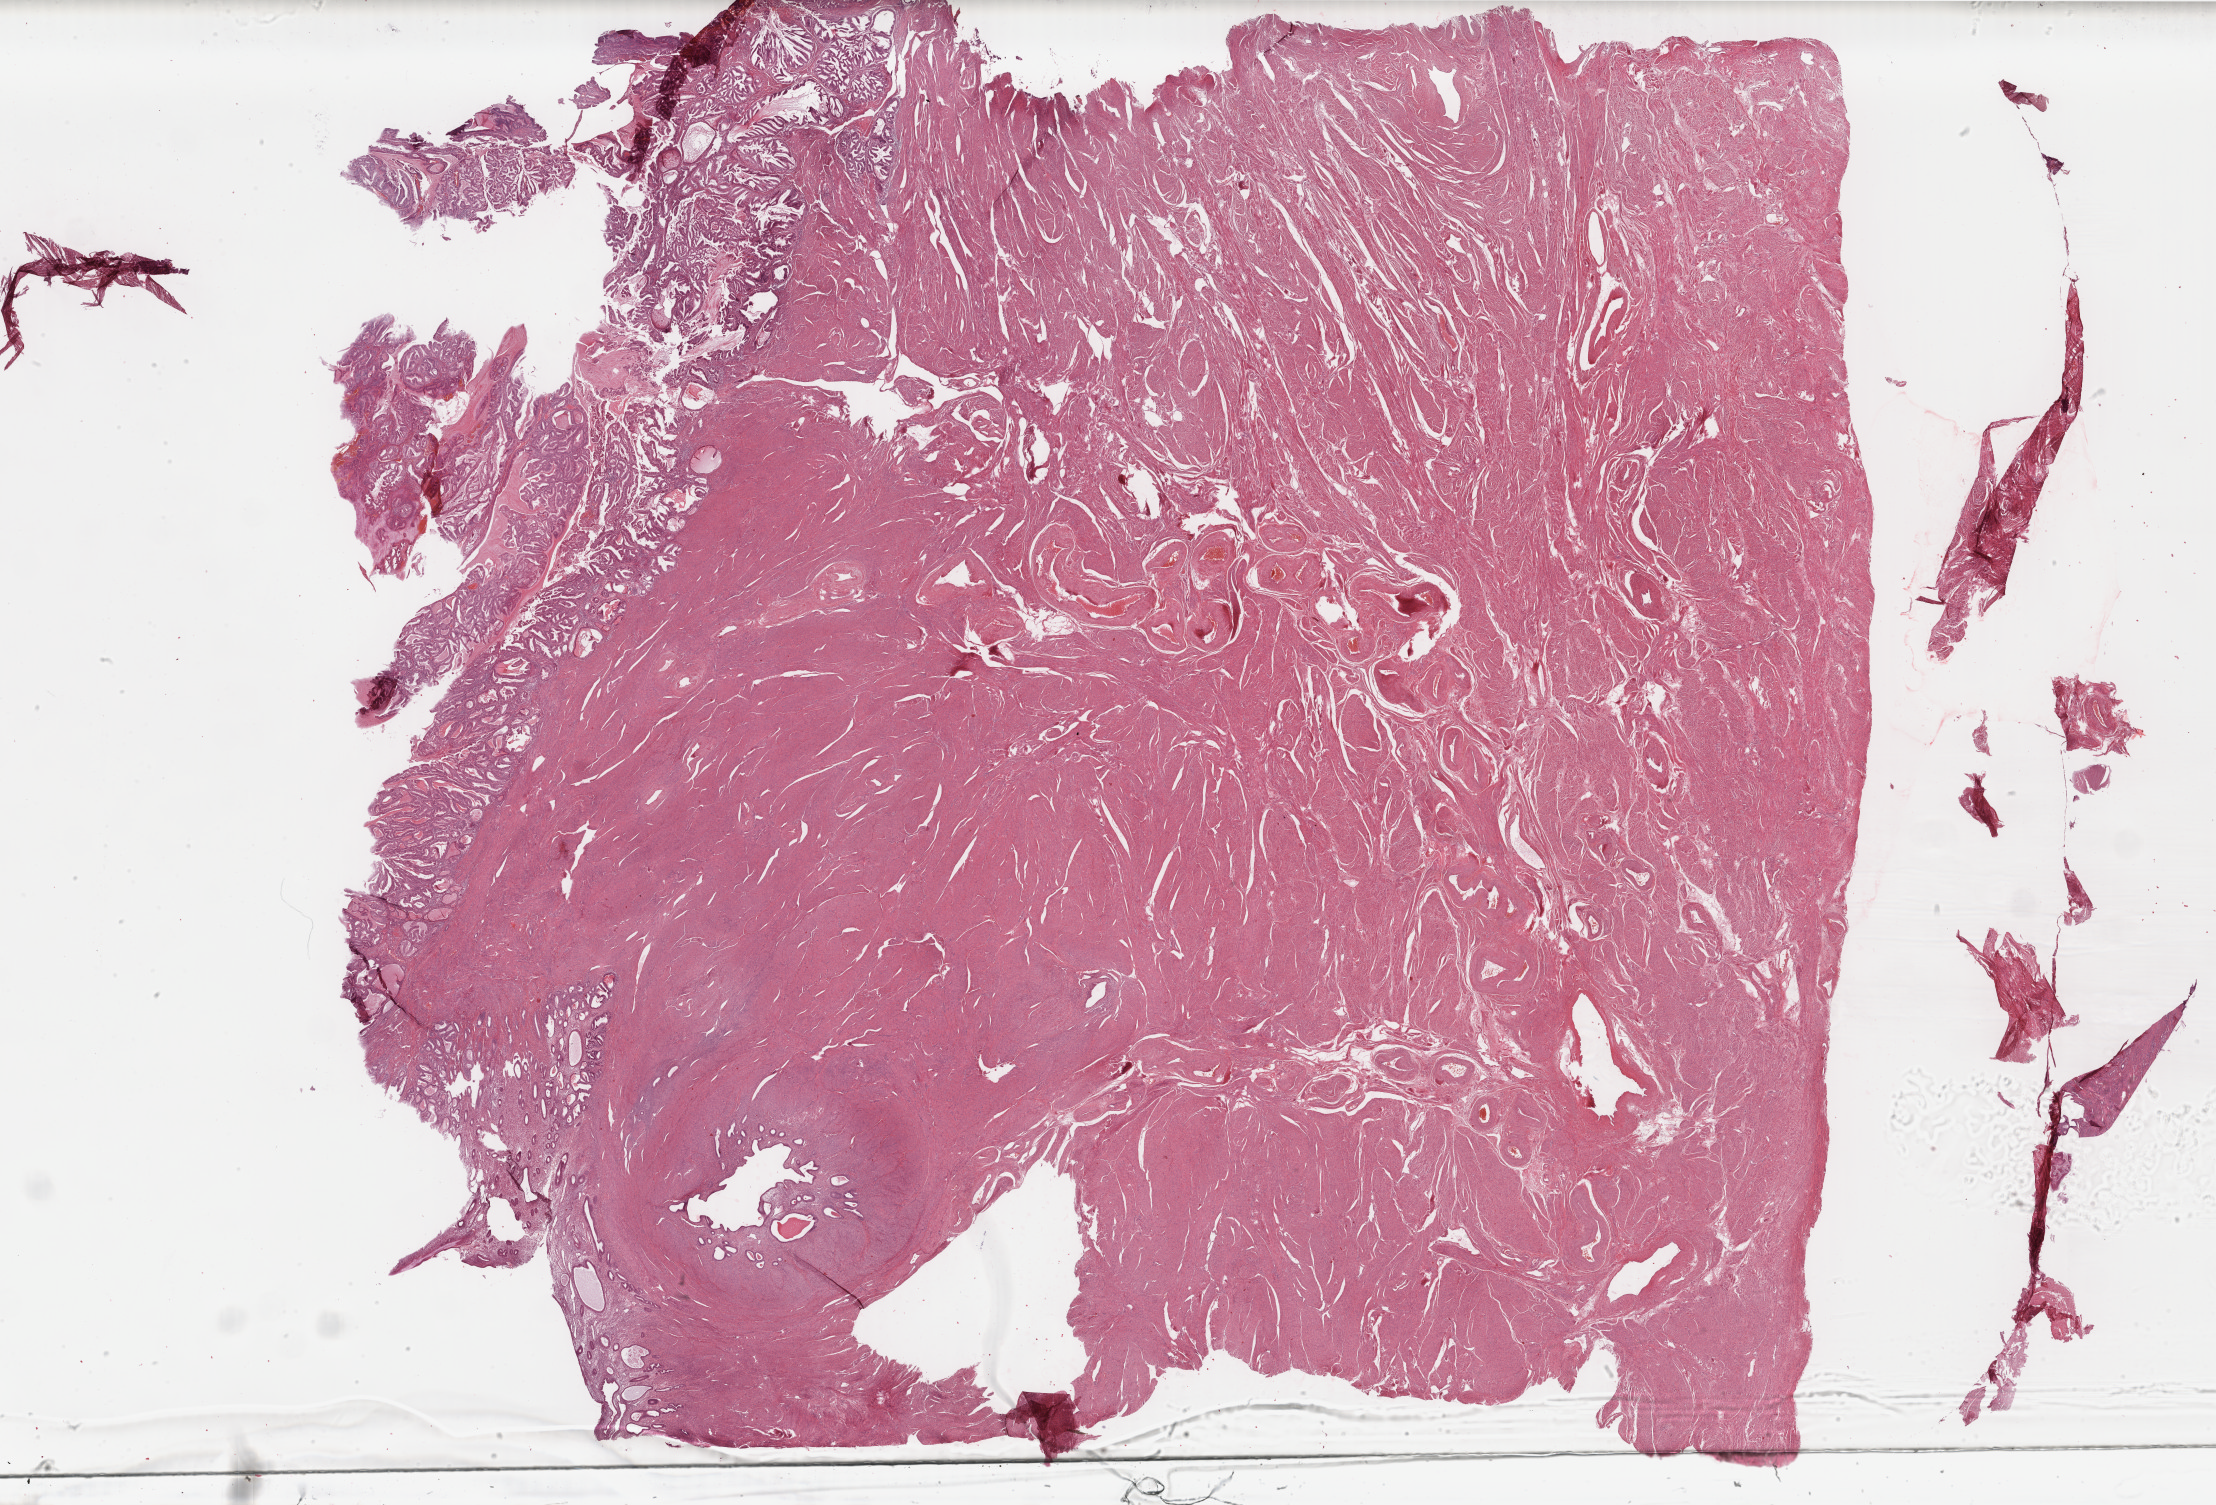
Hematoxylin and eosin (H&E) stained whole-slide image, a low-resolution overview of the entire scanned area, about 35.2 x 23.9 mm (slide scanned at 40x). Formalin-fixed paraffin-embedded (FFPE) diagnostic section. Primary tumour sample from the uterus. Female, age 56 years at initial diagnosis. Histologic grade: G1 (well differentiated).
Diagnosis: Endometrioid adenocarcinoma, NOS (endometrium). Lymph nodes positive (case pathology): 0 of 2 examined. FIGO stage: IB.